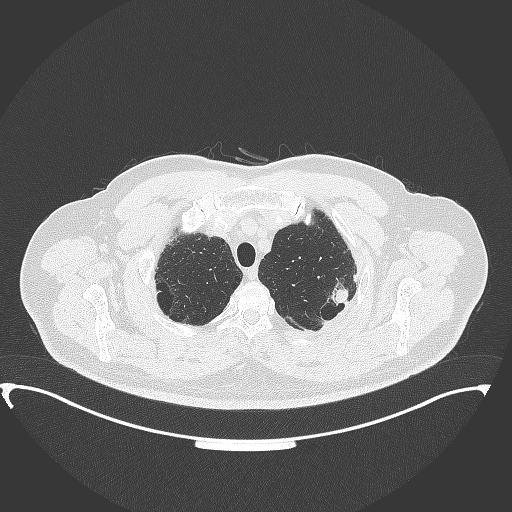
Chest CT, one axial slice; position 316 of 350 along the scan axis; reconstruction kernel B70f; 120 kVp; lung window (W 1500 / L -600 HU); 512 × 512 image matrix, field of view 459 × 459 mm. Patient: male, 64 years. From the clinical record (not read from this slice): clinical TNM (as recorded): T1c N1 M1.
Structures marked on this image (rectangle marked by the reading radiologist):
- lung tumour (recorded histology: adenocarcinoma): box from (x=329, y=283) to (x=353, y=307) px